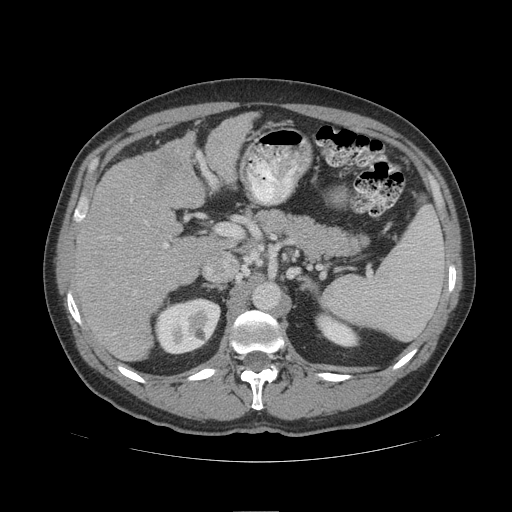
Contrast-enhanced abdominal CT (liver protocol), one axial slice. 140 kVp. Soft-tissue window (W 400 / L 40 HU). 2.5 mm slice thickness. 512 × 512 image matrix, field of view 420 × 420 mm. From the clinical record (not read from this slice): diagnosis: hepatocellular carcinoma (patient treated with transarterial chemoembolisation; whether this scan precedes or follows treatment is not stated here); TNM stage (as recorded): Stage-IIIB.
Structures marked on this image (semi-automatically segmented with operator editing):
- liver parenchyma outside the tumour (the mass and vessels are separate outlines, so this box may not span the whole liver): bounding box <74,112,255,360> (left, top, right, bottom; pixels)
- liver vessels: <119,153,211,248>